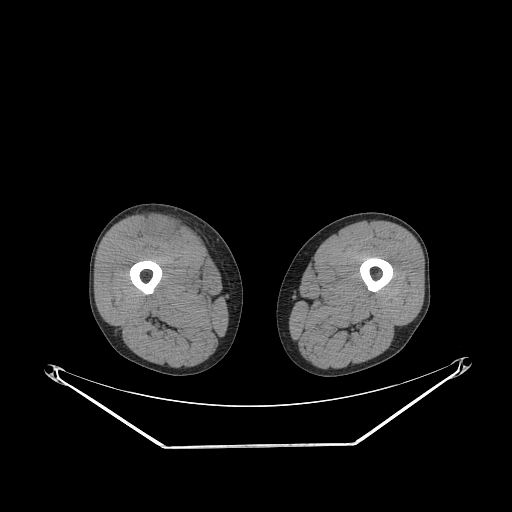
CT of an extremity soft-tissue mass (from a PET/CT study), one axial slice. Slice 246 of 311 in the series (ordered by position). 140 kVp. Soft-tissue window (W 400 / L 40 HU). 3.75 mm slice thickness. 512 × 512 image matrix. Male patient. Case-level facts recorded for this patient, not image findings: histological type: pleiomorphic leiomyosarcoma; grade: intermediate; site of the primary tumour: right thigh.
Annotated regions visible in this slice (expert contour drawn on MRI and transferred to this co-registered scan by the dataset authors):
- gross tumour volume including surrounding oedema: box from (x=146, y=217) to (x=179, y=241) px